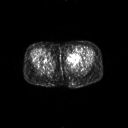
FDG PET of an extremity soft-tissue mass (from a PET/CT study), one axial slice. Slice 15 of 267 in the series (ordered by position). 3.27 mm slice thickness. 128 × 128 image matrix. Patient: female, 47 years. Case-level facts recorded for this patient, not image findings: histological type: myxofibrosarcoma; grade: intermediate; site of the primary tumour: left thigh.
Outlined on this slice (expert contour drawn on MRI and transferred to this co-registered scan by the dataset authors):
- gross tumour volume including surrounding oedema: box from (x=67, y=53) to (x=82, y=62) px
- gross tumour volume (mass): (x=70, y=53)–(x=79, y=59)